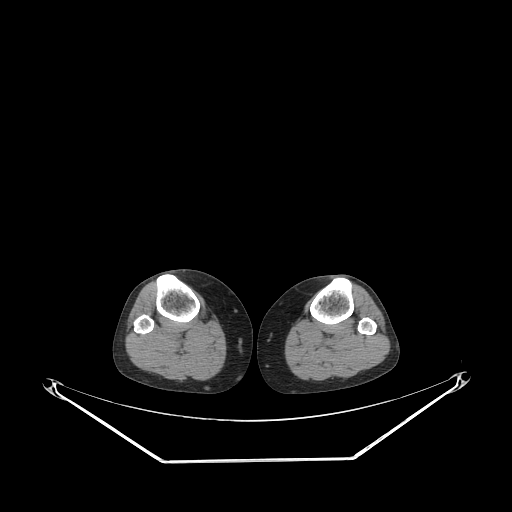
CT of an extremity soft-tissue mass (from a PET/CT study), one axial slice. Slice 159 of 267 in the series (ordered by position). Reconstruction kernel STANDARD. Soft-tissue window (W 400 / L 40 HU). 3.75 mm slice thickness. 512 × 512 image matrix. Female patient. From the clinical record (not read from this slice): histological type: undifferentiated – high grade; grade: high; site of the primary tumour: right thigh.
Annotated regions visible in this slice (expert contour drawn on MRI and transferred to this co-registered scan by the dataset authors):
- gross tumour volume (mass): bounding box [x1, y1, x2, y2] px = [201, 315, 207, 321]